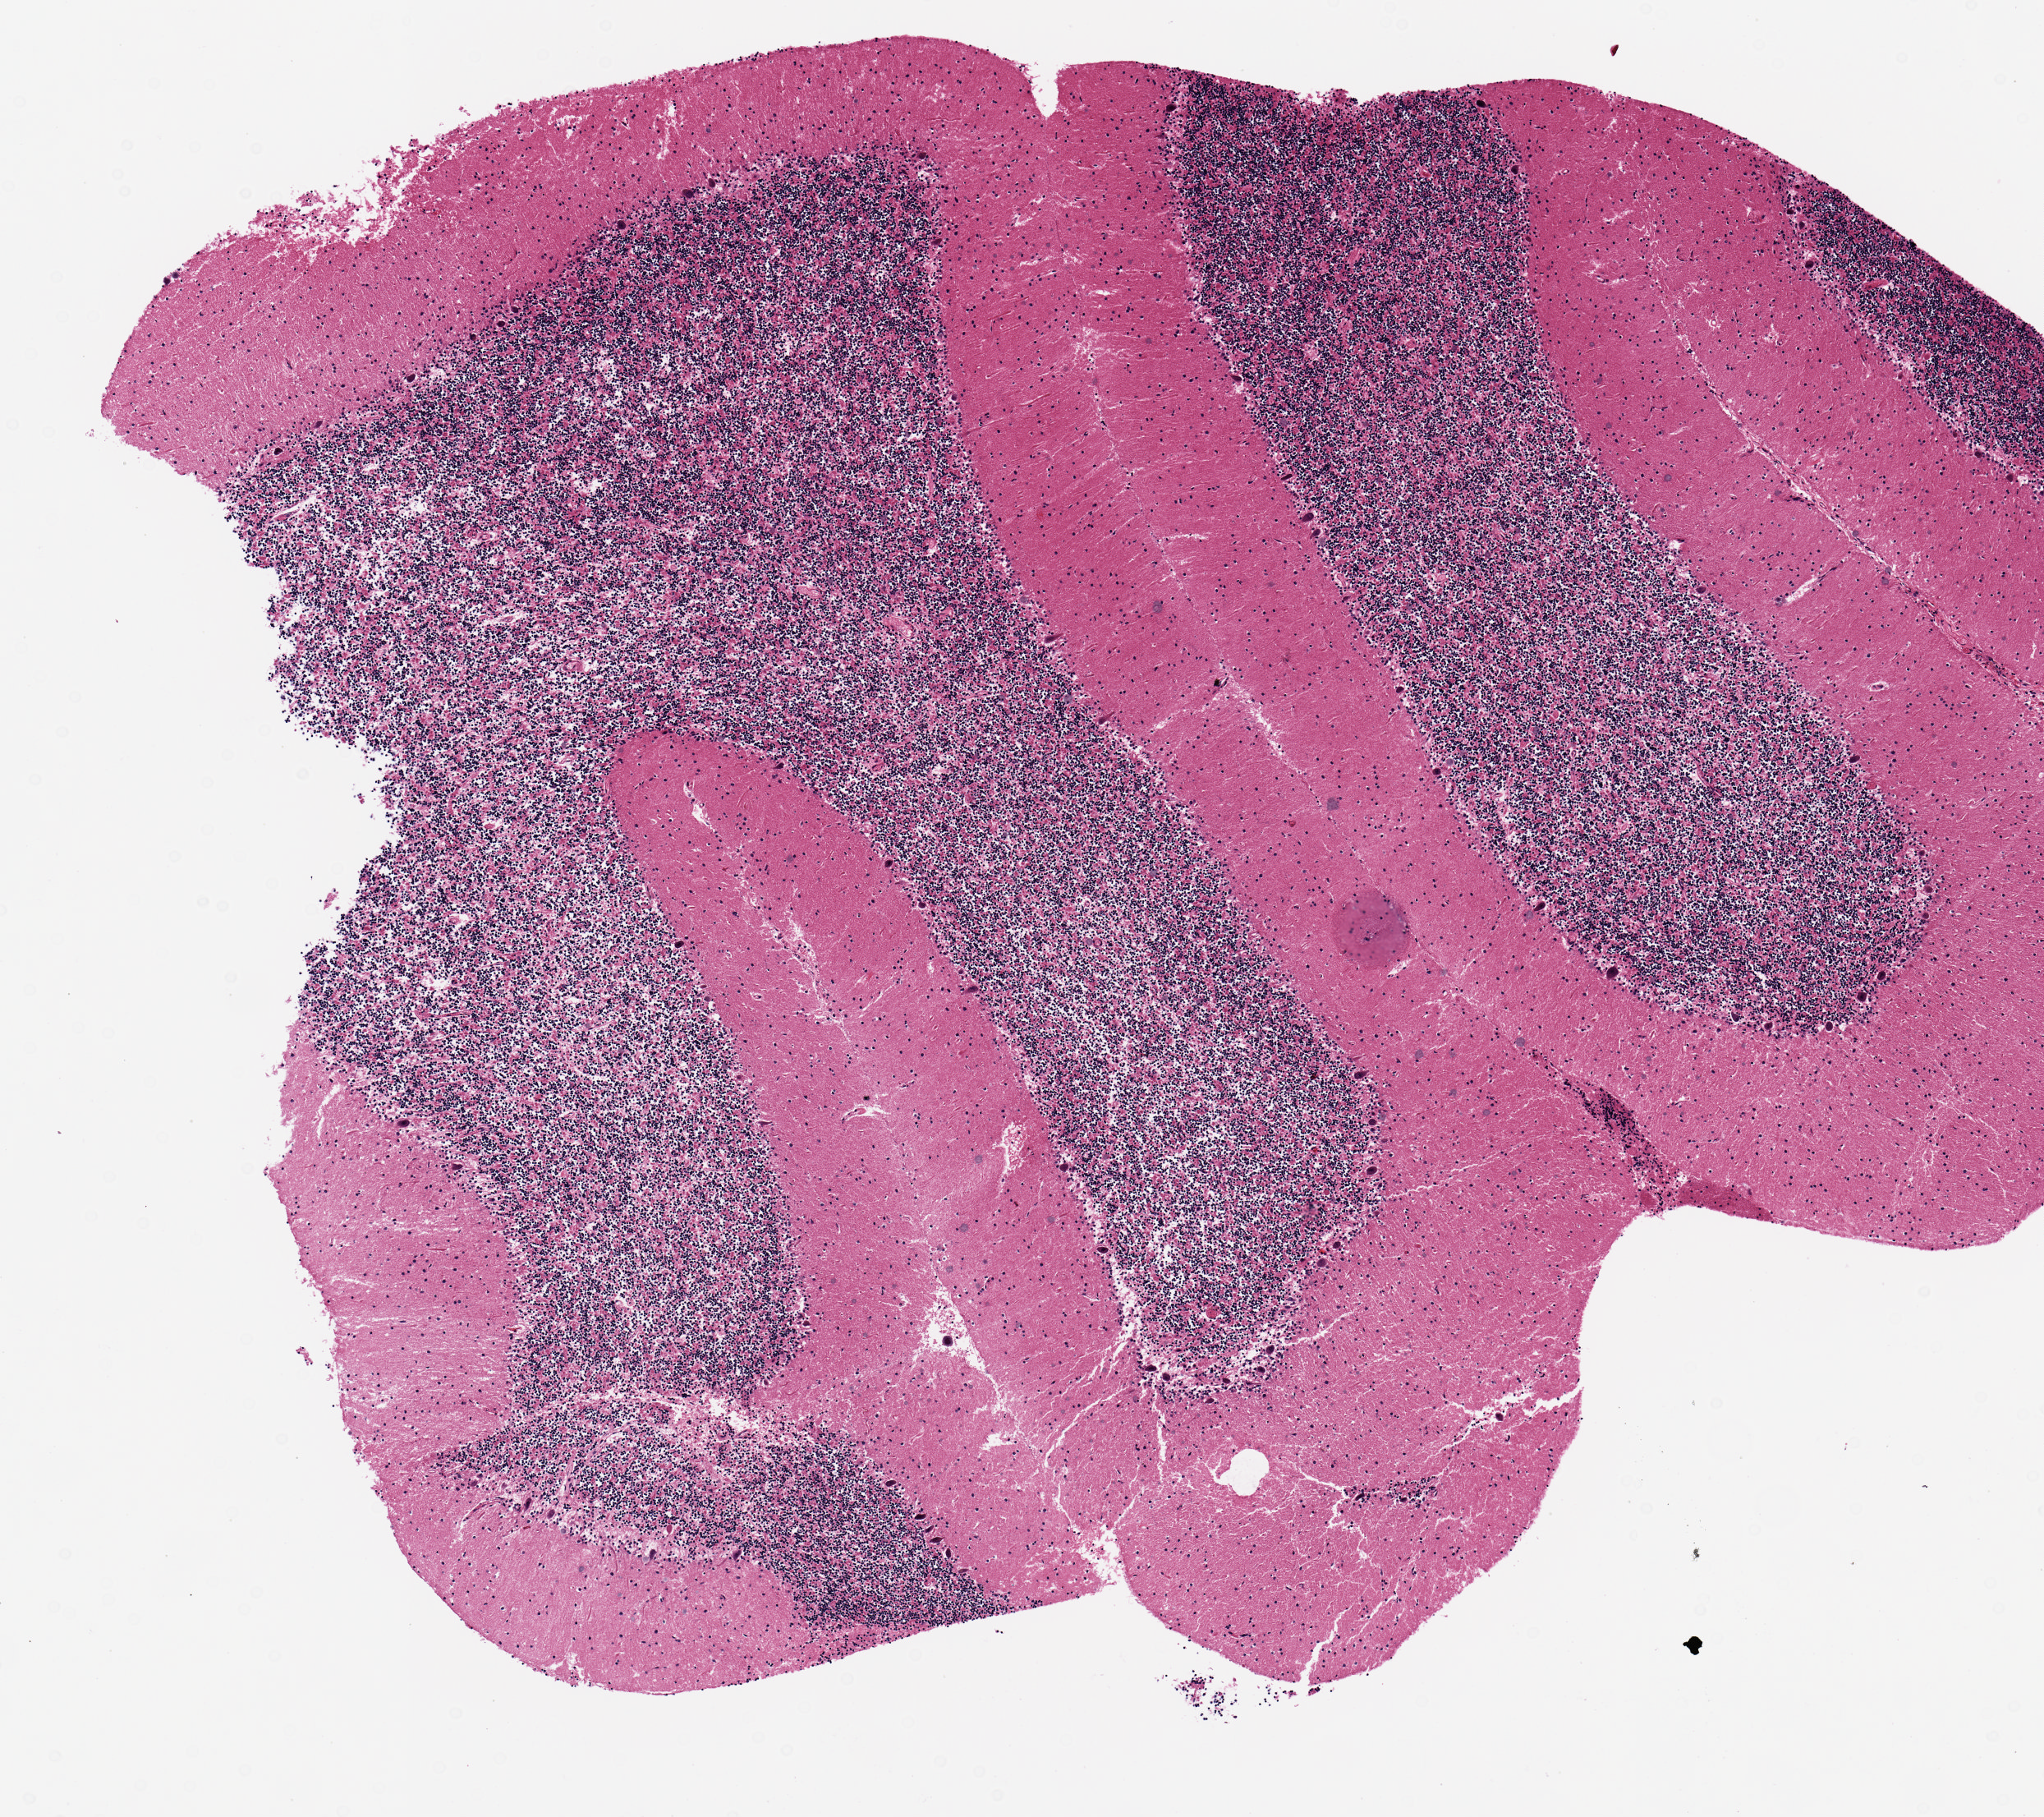
Digitized haematoxylin and eosin-stained section, brightfield — a low-resolution overview of the entire scanned area, about 4.9 x 4.4 mm. PAXgene-fixed, paraffin-embedded tissue. Sampled site (target tissue): cerebellum. Donor tissue sample. Donor: male.
• pathologist's review note for this sample: 1 piece 4x4 mm